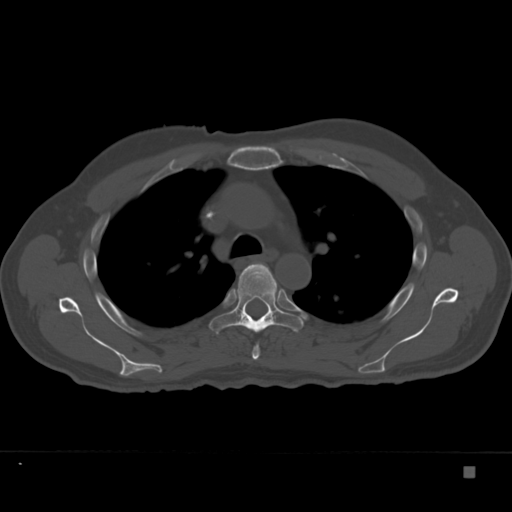
CT including the spine, one axial slice; position 260 of 332 along the scan axis; 120 kVp; bone window (W 1800 / L 400 HU); 1.5 mm slice thickness; 512 × 512 image matrix, field of view 389 × 389 mm. Patient: male, 72 years. Case-level facts recorded for this patient, not image findings: primary cancer: skeletal.
Annotated regions visible in this slice (semi-automatically segmented with operator editing):
- T4 vertebra: bounding box (x1, y1, x2, y2) in pixels: (252, 290, 280, 360)
- T5 vertebra: (209, 263, 304, 334)